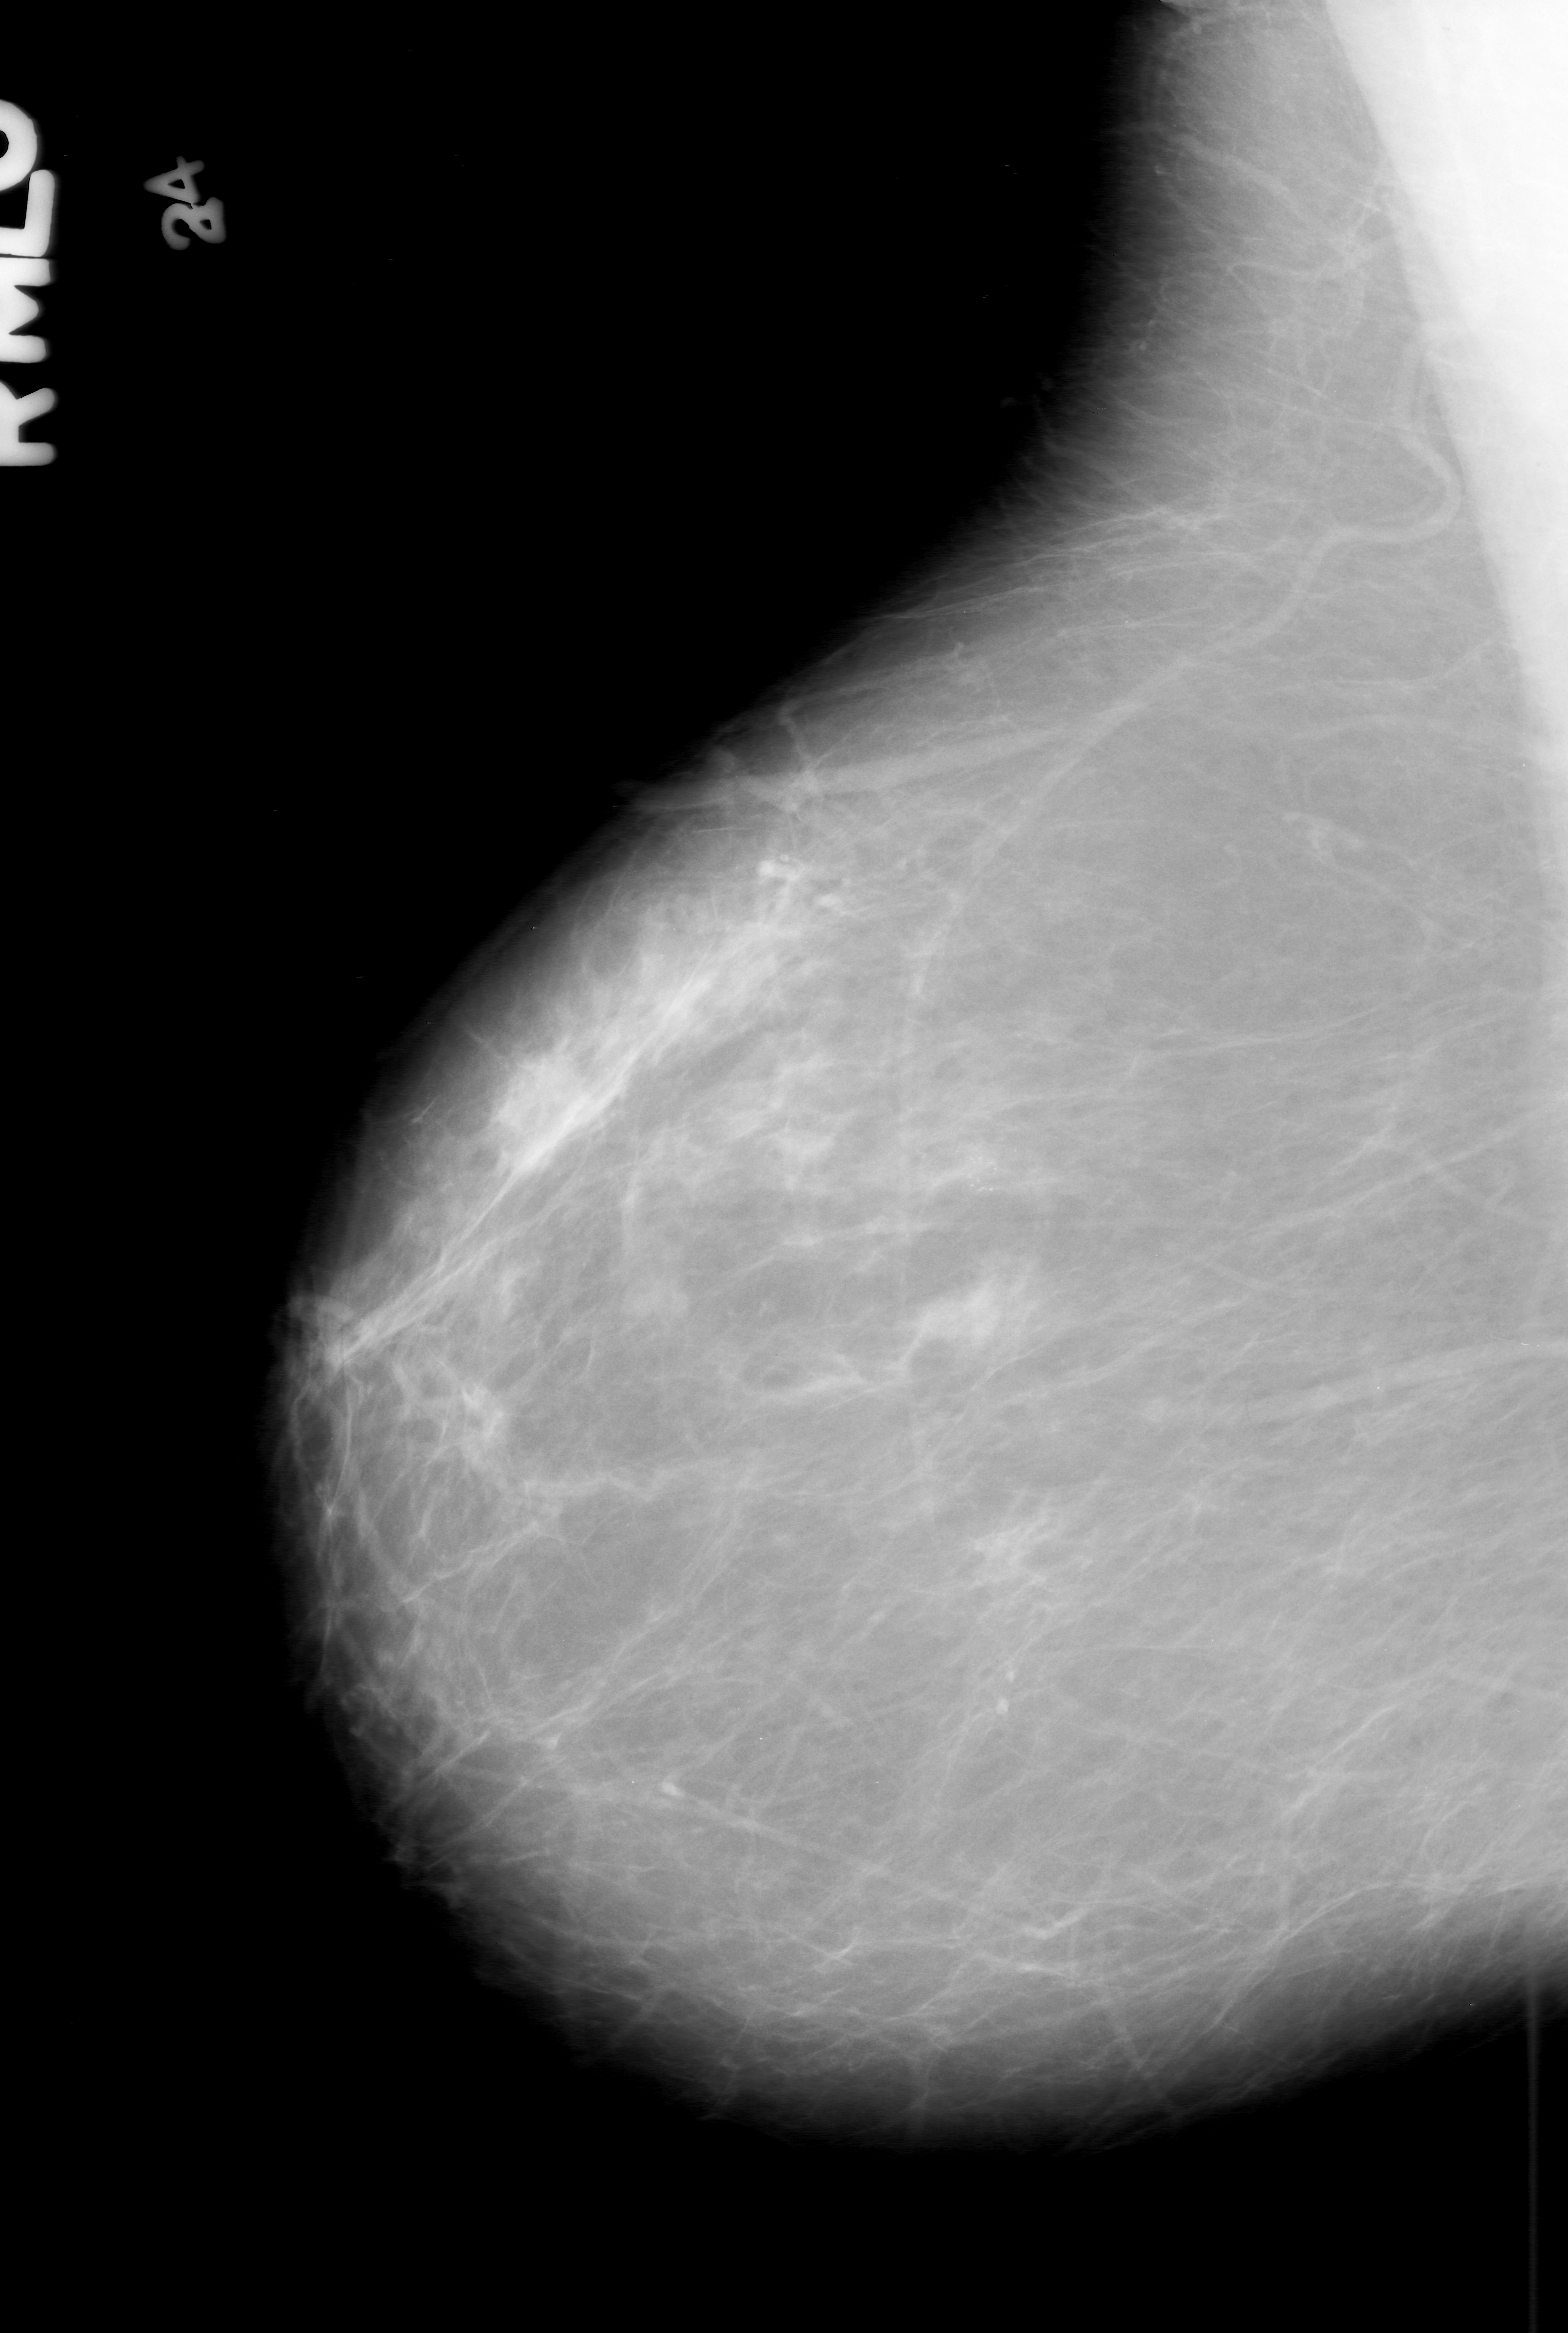
Scanned film-screen mammogram, right breast, mediolateral oblique (MLO) view, breast composition: scattered fibroglandular densities (BI-RADS density category 2 of 4).
- Marked findings (only marked abnormalities are described; nothing is implied about the rest of the image): calcifications, morphology pleomorphic, distribution clustered; BI-RADS assessment category 0; pathology (as recorded): benign.